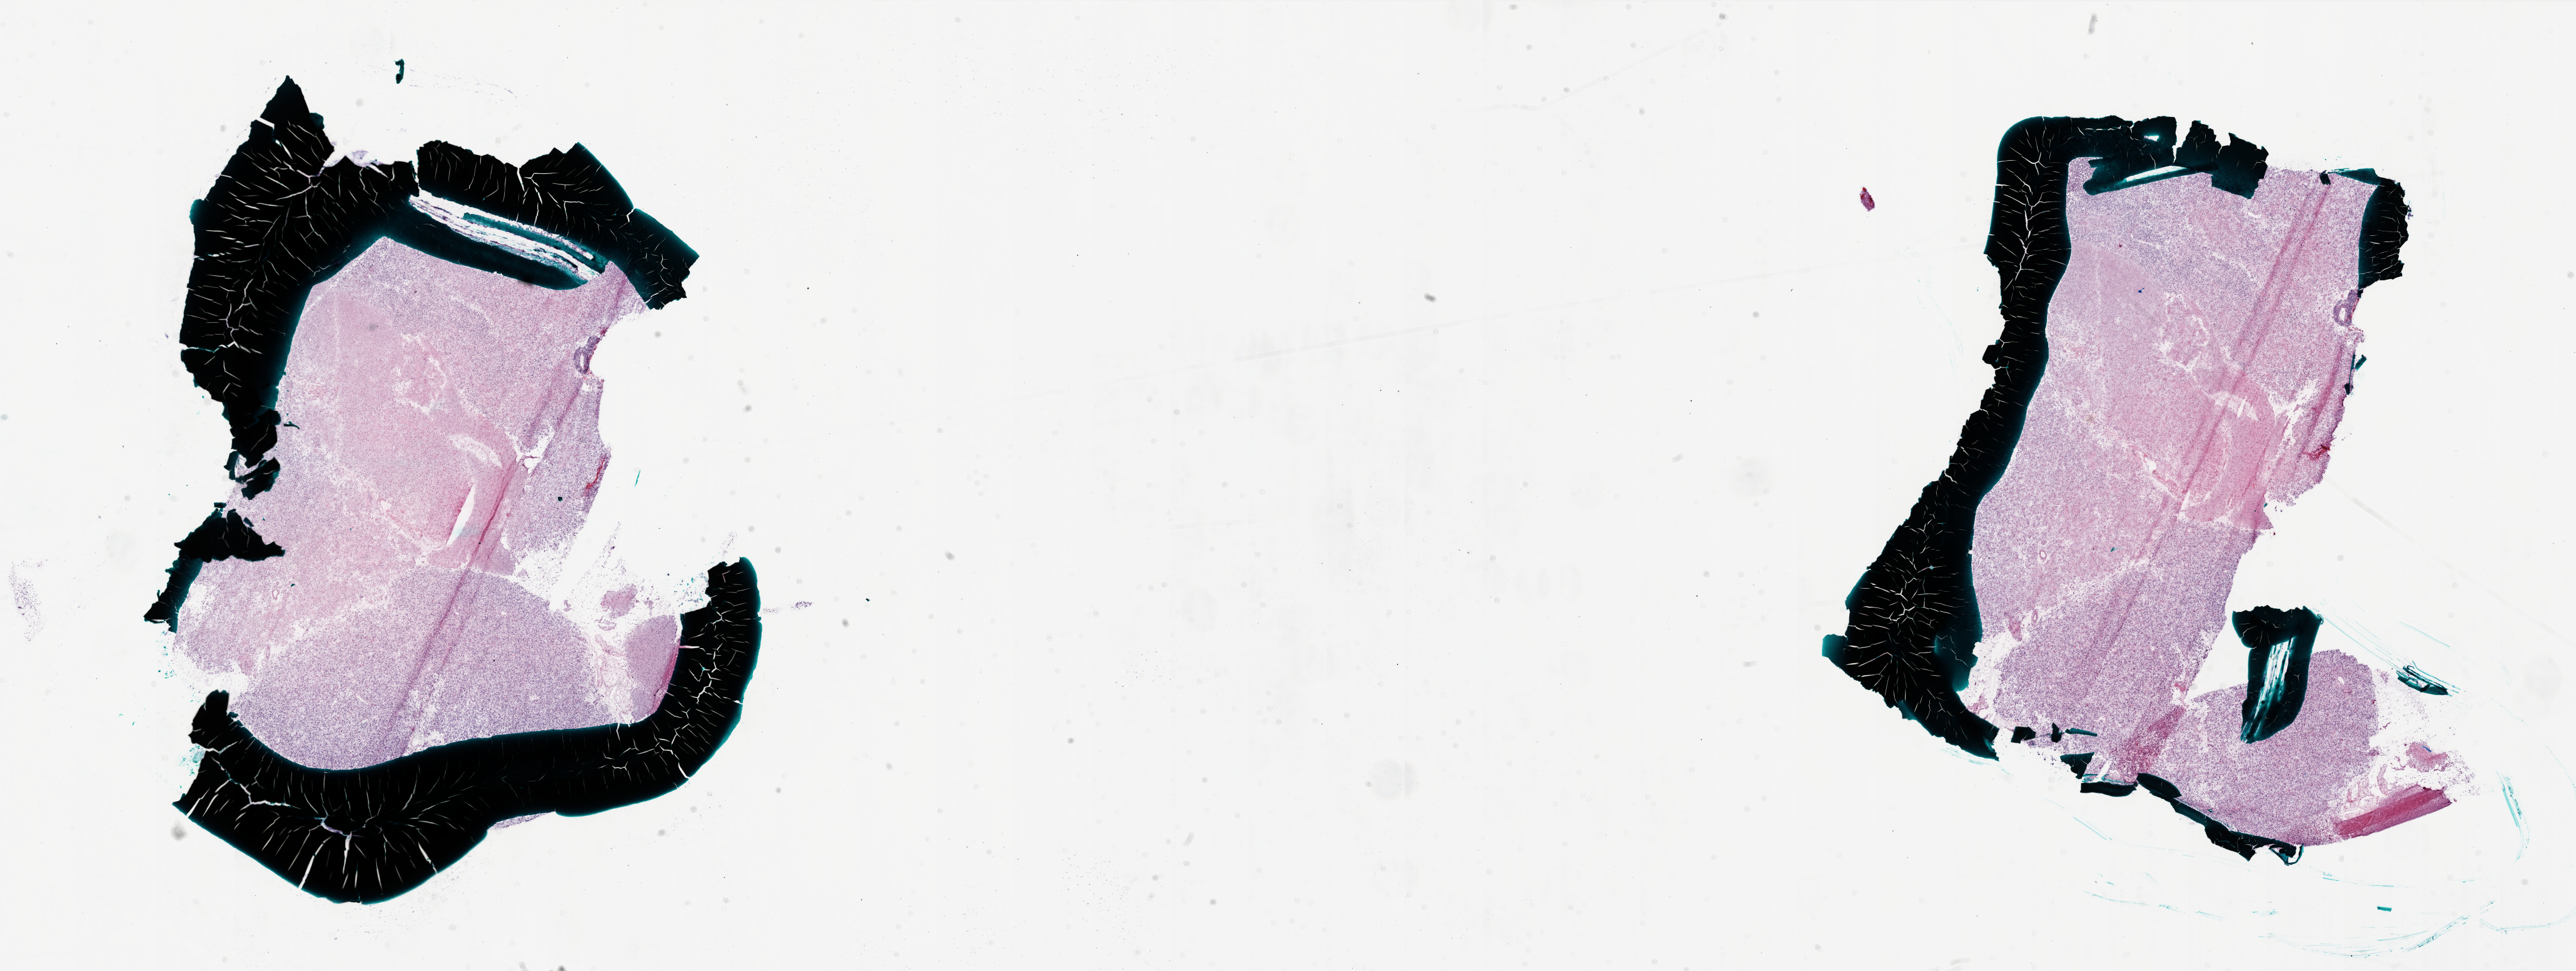
Digitized Hematoxylin and eosin (H&E) stained tissue section (whole slide) — low-resolution overview of the scanned area, about 33.0 x 12.4 mm (from a 20x scan); frozen section from the bottom of the tissue portion; primary tumour sample from the brain. Male, age 31 years at initial diagnosis. Slide review estimates, as recorded: tumour cells 90%, tumour nuclei 100%, normal cells 0%, stromal cells 0%, necrosis 10%.
Histologic diagnosis: Glioblastoma.